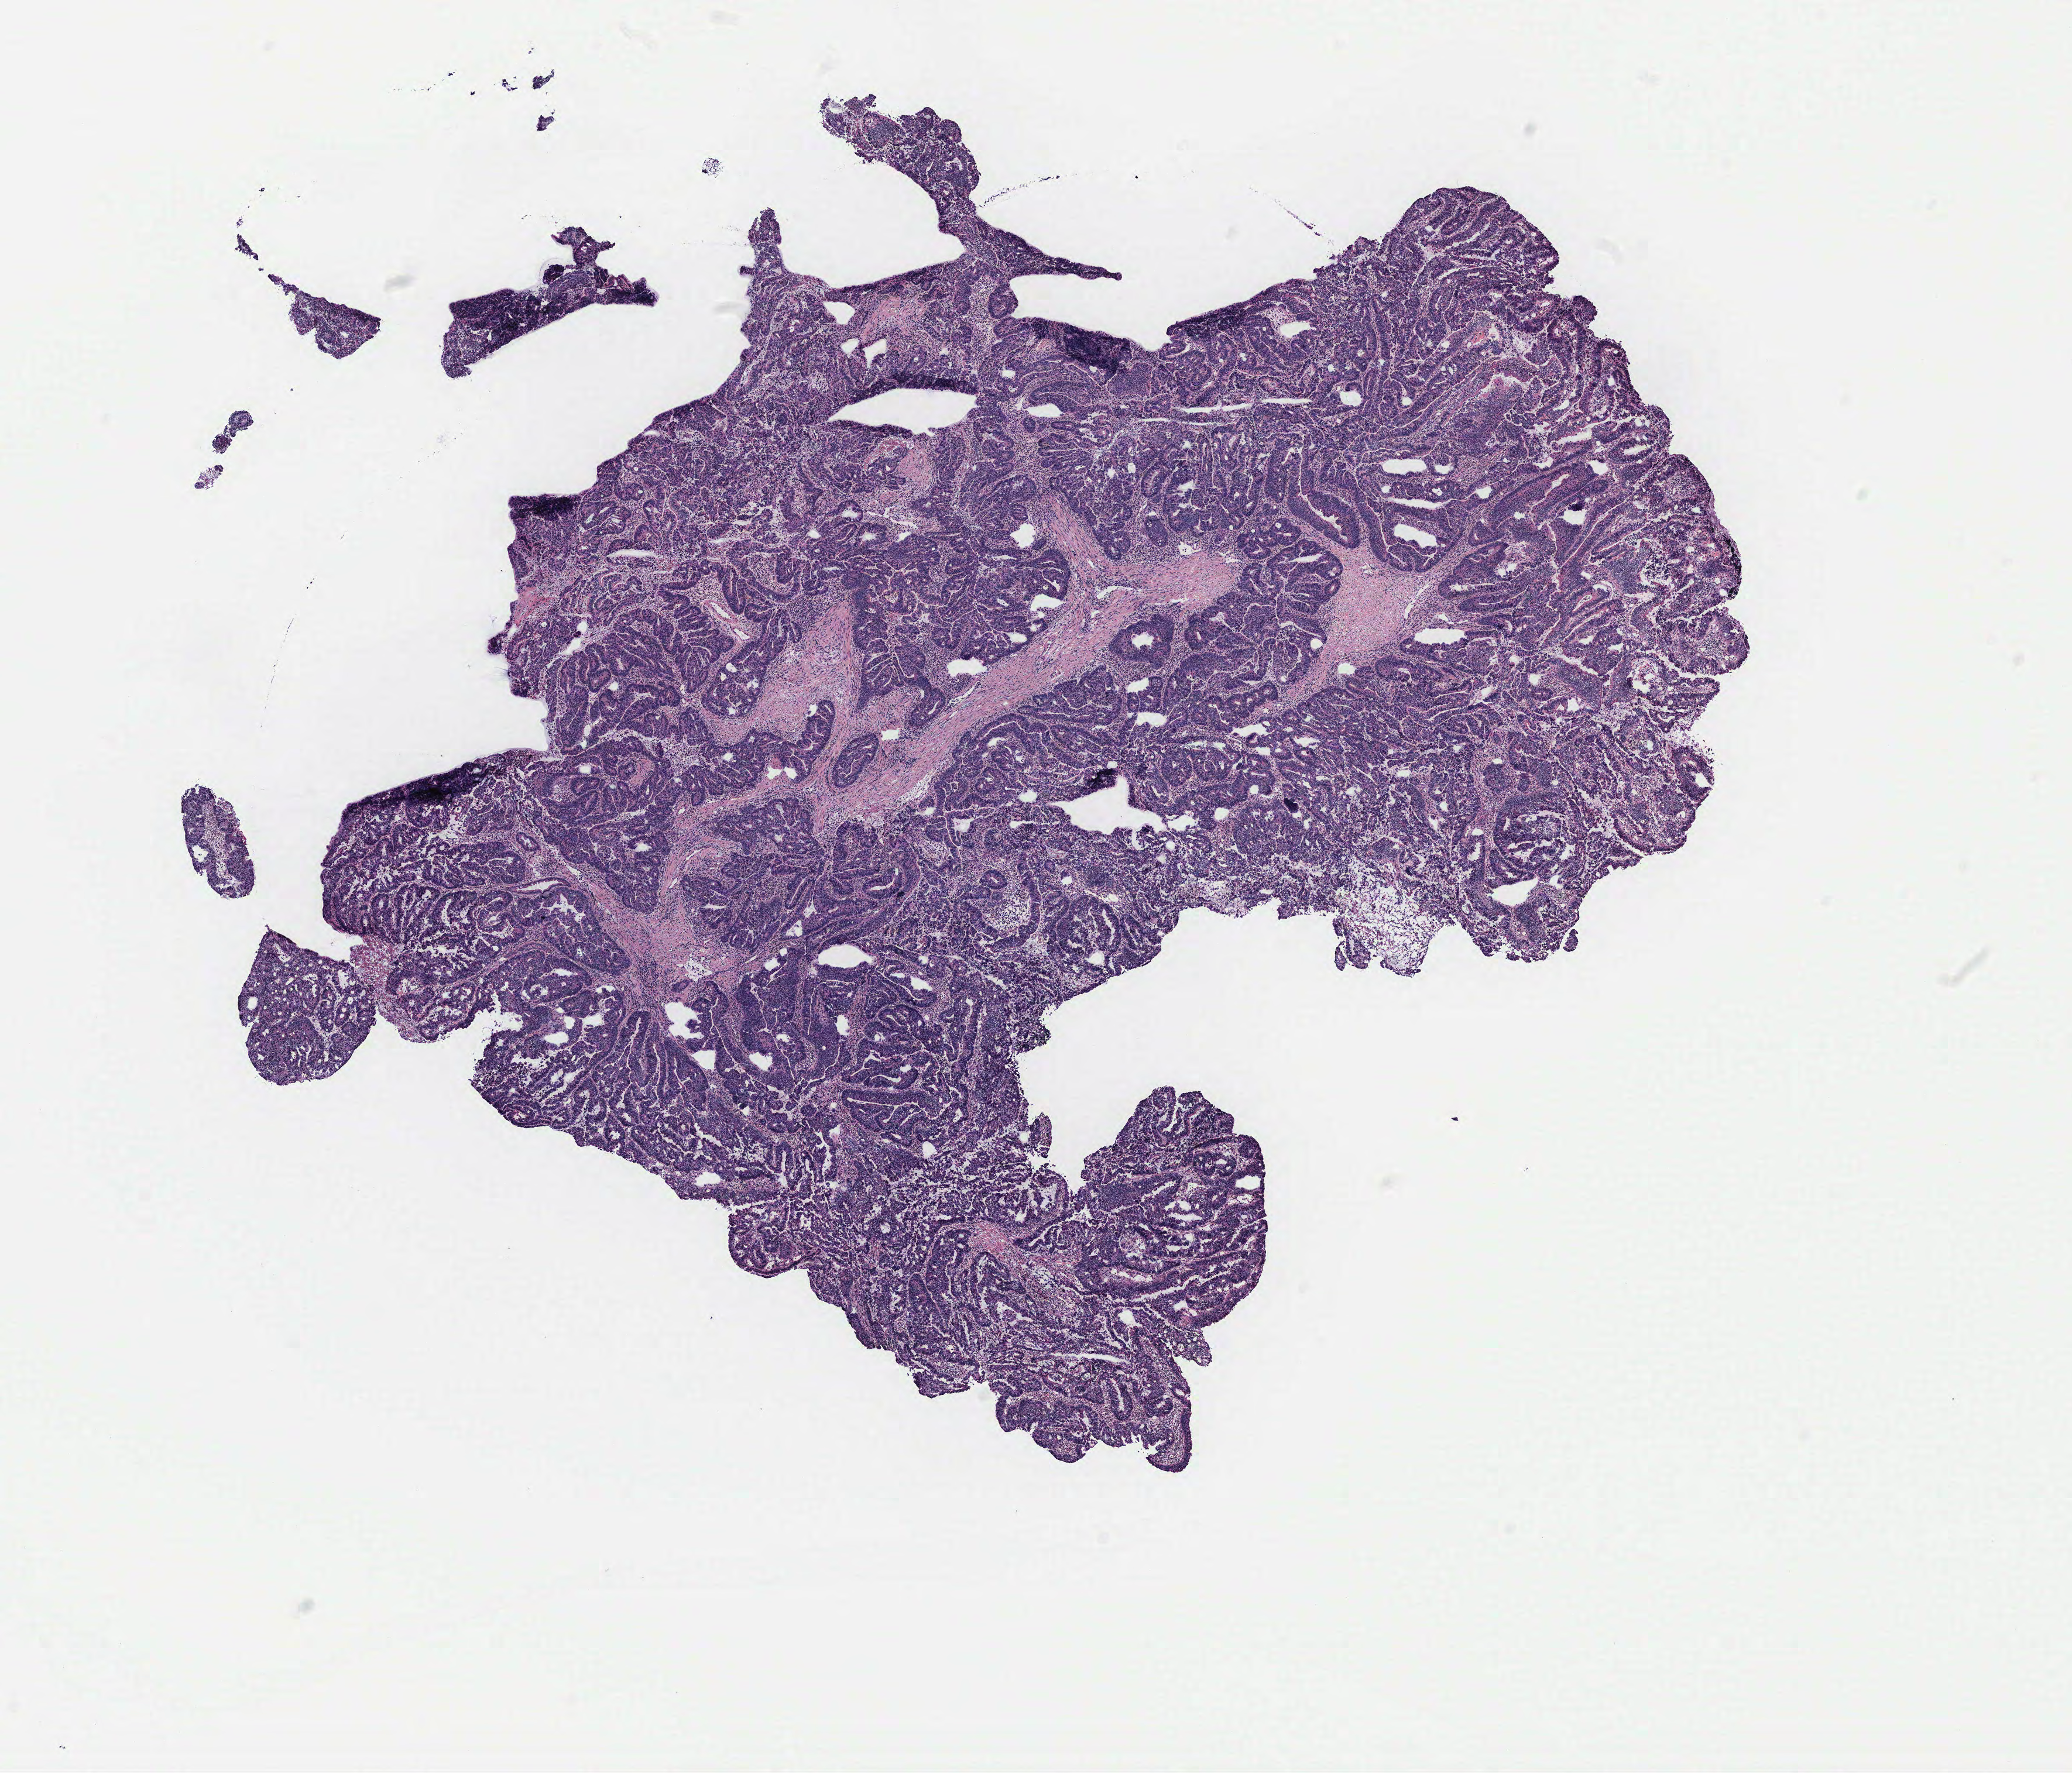
H&E whole-slide image — low-resolution overview of the scanned area, about 14.2 x 12.1 mm, normal (non-tumour) tissue sample, colon. Patient: male, age 62 years.
This section: normal (non-tumour) tissue from the same patient. Patient diagnosis: Adenocarcinoma, NOS.